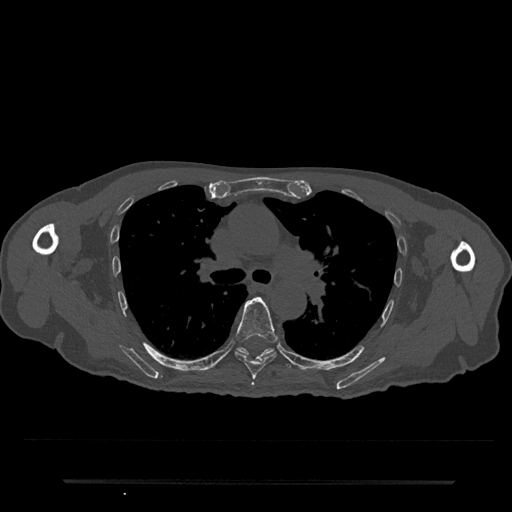
CT including the spine, one axial slice; slice 519 of 797 in the series (ordered by position); 120 kVp; bone window (W 1800 / L 400 HU); 0.5 mm slice thickness; 512 × 512 image matrix, field of view 427 × 427 mm. Male patient, age 74 years. Case-level facts recorded for this patient, not image findings: primary cancer: prostate.
Annotated regions visible in this slice (semi-automatic segmentation, software-assisted and operator-edited):
- T5 vertebra: bounding box <252,382,254,385> (left, top, right, bottom; pixels)
- T6 vertebra: <235,297,278,380>
- T7 vertebra: <237,347,291,368>